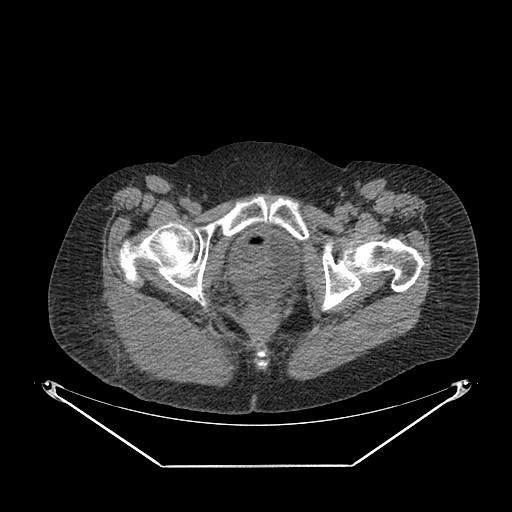
CT of an extremity soft-tissue mass (from a PET/CT study), one axial slice; slice 50 of 267 in the series (ordered by position); reconstruction kernel SOFT; 140 kVp; soft-tissue window (W 400 / L 40 HU); 512 × 512 image matrix, field of view 500 × 500 mm. Female patient. Case-level facts recorded for this patient, not image findings: histological type: spindle cell suggestive of myxofibrosarcoma; grade: intermediate; site of the primary tumour: right buttock.
Outlined on this slice (expert contour drawn on MRI and transferred to this co-registered scan by the dataset authors):
- gross tumour volume (mass): bounding box [x1, y1, x2, y2] px = [105, 297, 202, 371]